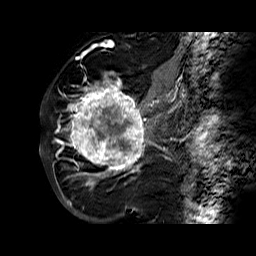
Breast MRI (dynamic contrast-enhanced), one sagittal slice. Position 38 of 60 along the scan axis. Dynamic contrast-enhanced series, time point 2 of 6 at this slice position (early post-contrast). 1.5 T. TE 6.3 ms, TR 32.4 ms. 256 × 256 image matrix, field of view 200 × 200 mm. Female patient. Case-level facts recorded for this patient, not image findings: setting: breast cancer imaged before/during neoadjuvant chemotherapy; receptor status: HR-positive, HER2-negative.
Structures marked on this image (semi-automatic segmentation, software-assisted and operator-edited):
- analysis volume of interest (the breast-tissue region the enhancement analysis was run in; not a lesion): box from (x=68, y=72) to (x=177, y=183) px
- tumour enhancement mask (voxels above the 100 % enhancement threshold inside the analysis volume of interest): (x=68, y=72)–(x=171, y=183)